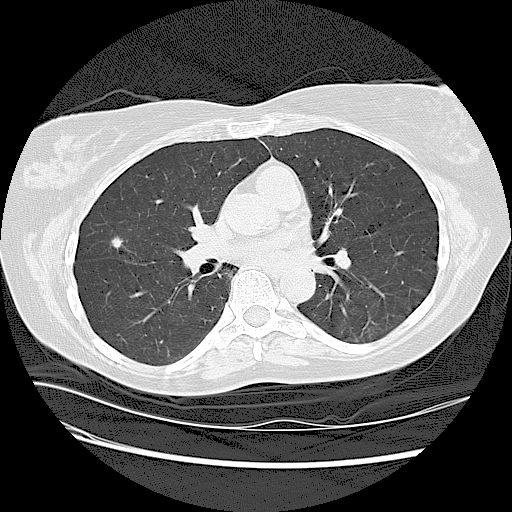
Low-dose screening chest CT, axial slice, baseline annual screen, lung window (W 1500 / L -600 HU), lung (sharp) reconstruction kernel (LUNG), 120 kVp. Female, age 63 years at enrolment. Current smoker at enrolment.
Expert-annotated lung lesion, bounding box (x1, y1, x2, y2) in pixels: (96, 226, 140, 265). Screening reader's record for this exam (one nodule recorded; not confirmed to be the boxed lesion): non-calcified nodule or mass ≥4 mm, right upper lobe, 7 × 7 mm, spiculated (stellate) margins, soft tissue attenuation. Official screen result: positive, change unspecified: nodule(s) >= 4 mm or enlarging nodule(s), mass(es), or other non-specific abnormalities suspicious for lung cancer.